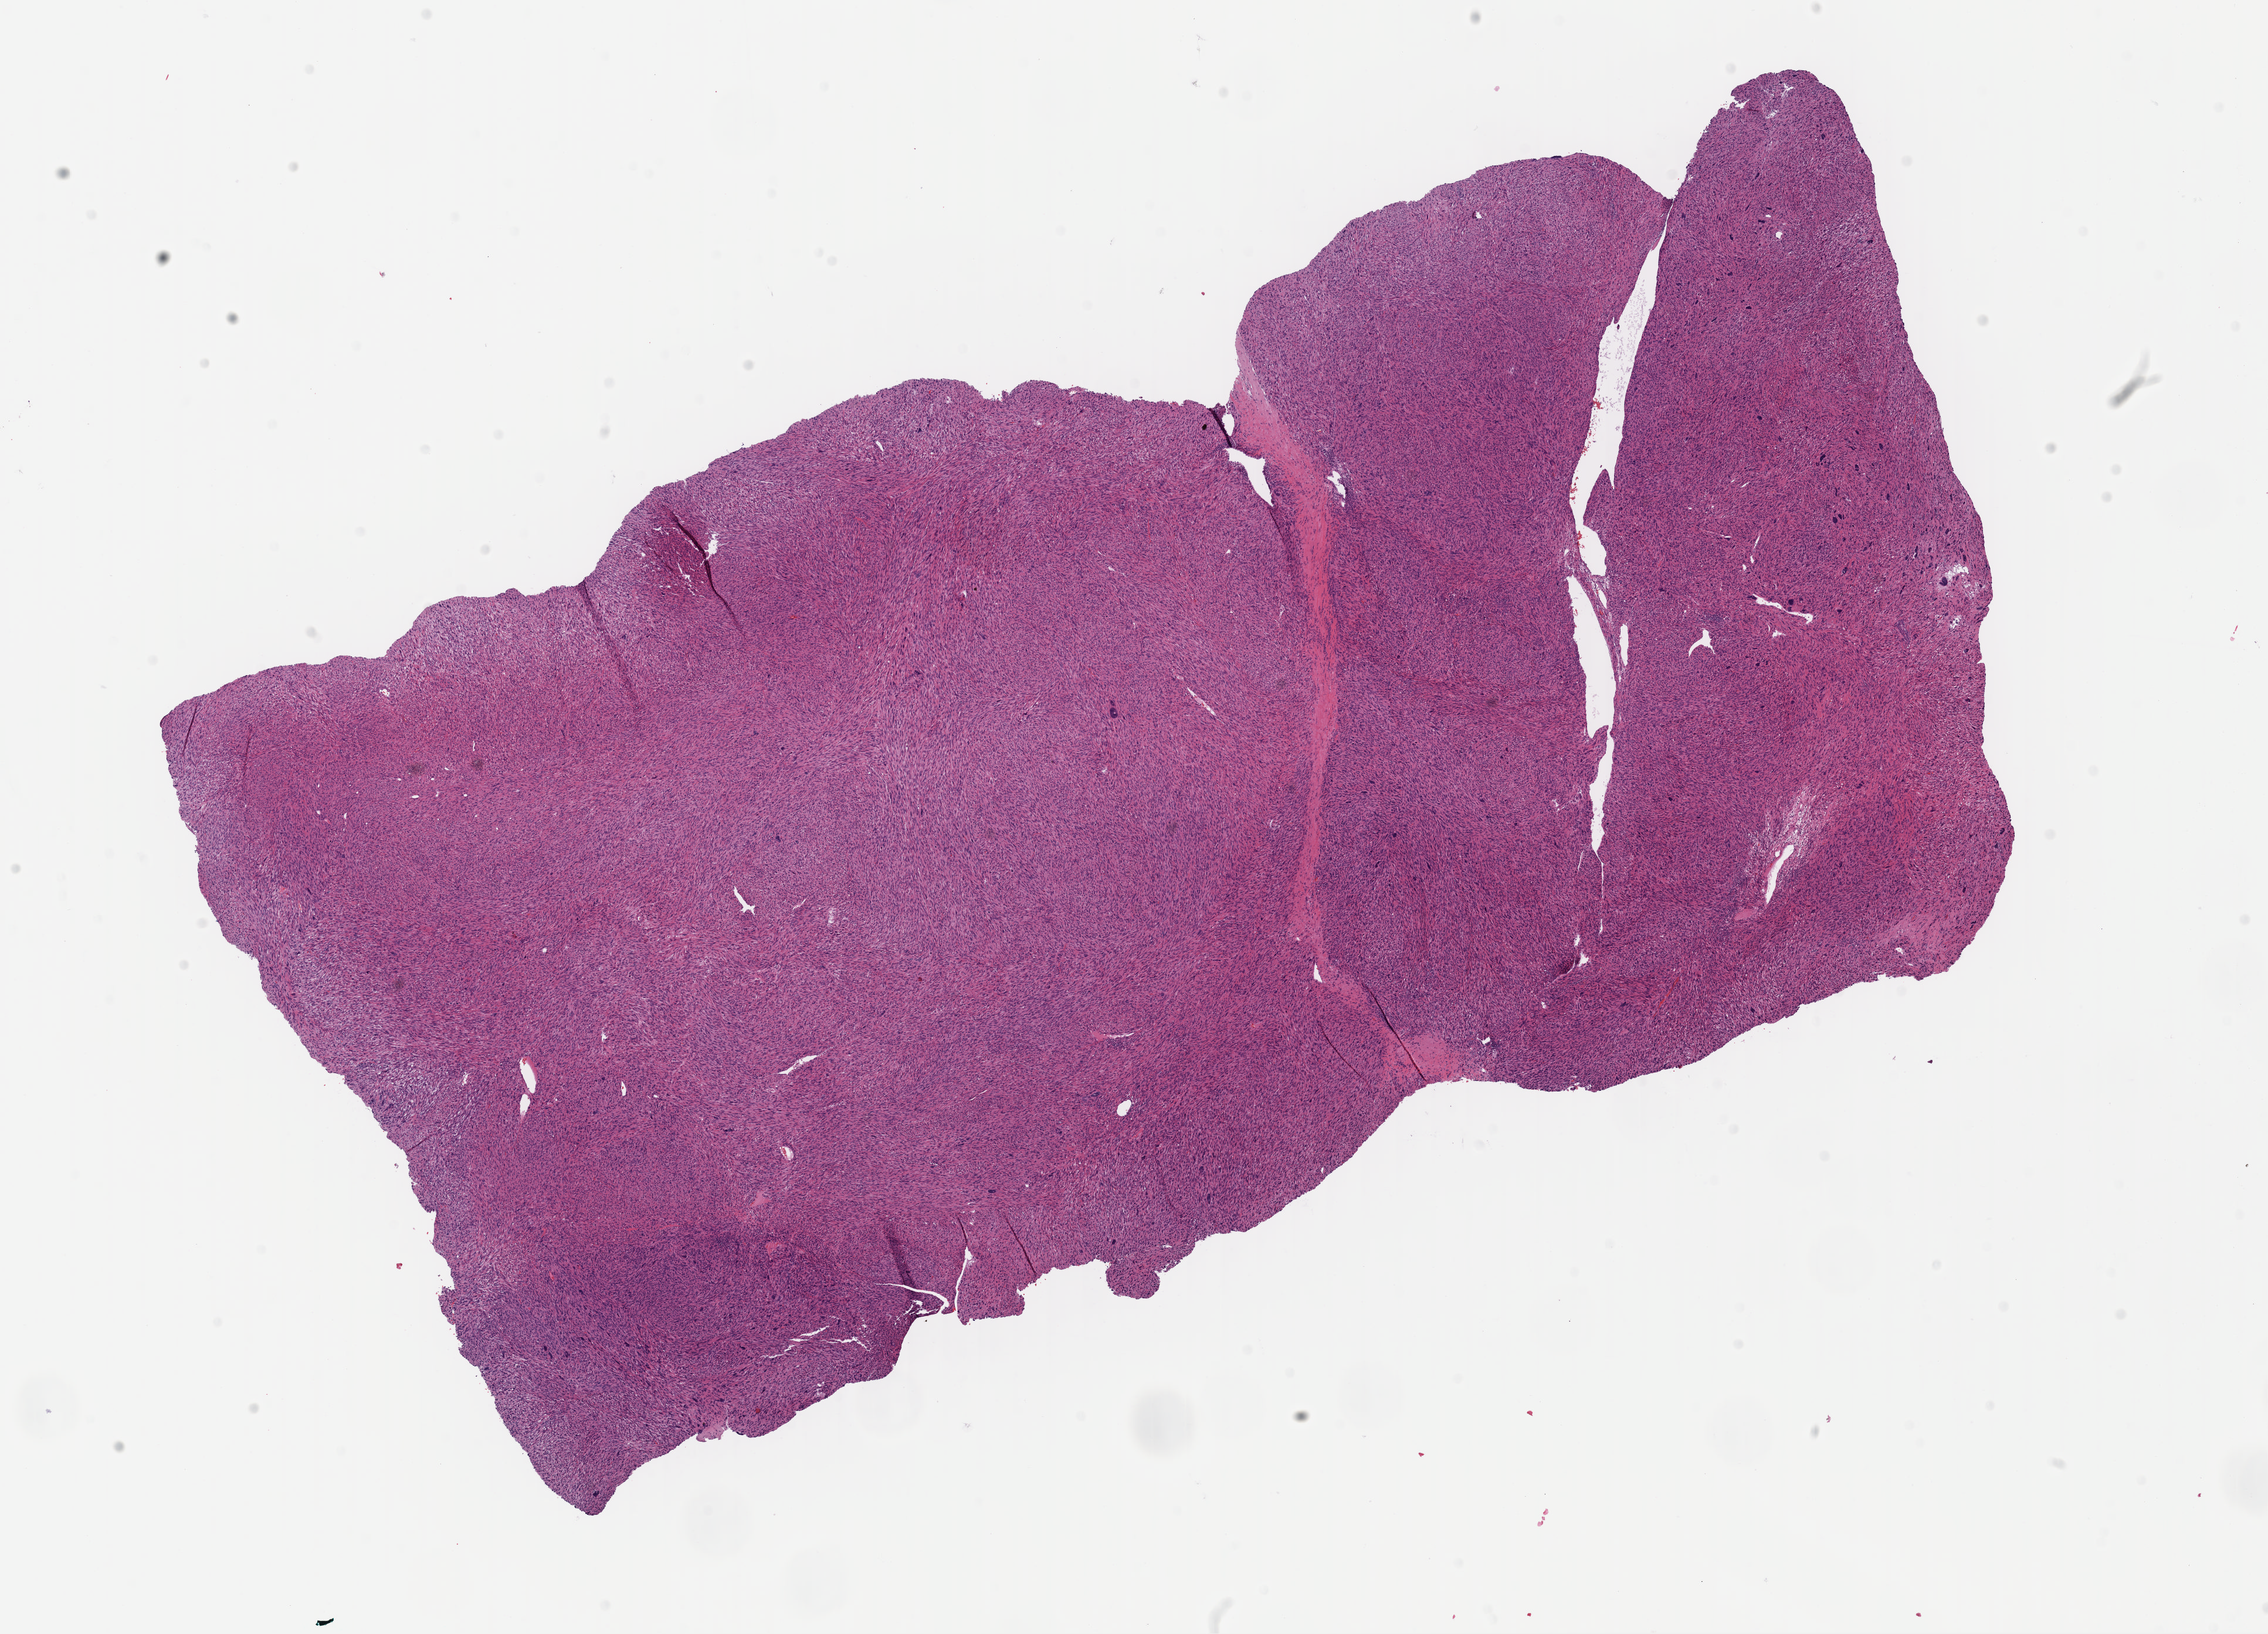
Whole-slide histology image, H&E-stained — whole scanned area (about 15.3 x 11.0 mm, from a 40x scan) shown as a low-resolution overview. Formalin-fixed paraffin-embedded (FFPE) diagnostic section. Primary tumour sample from the connective, subcutaneous and other soft tissues. Male, age 42 years at initial diagnosis.
- histologic diagnosis: Leiomyosarcoma, NOS